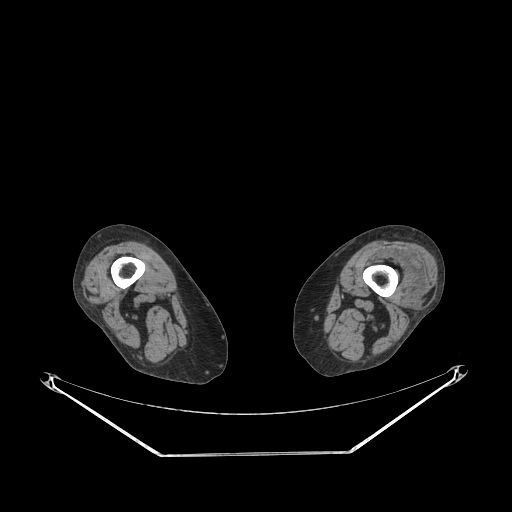
CT of an extremity soft-tissue mass (from a PET/CT study), one axial slice; slice 193 of 267 in the series (ordered by position); reconstruction kernel STANDARD; 140 kVp; soft-tissue window (W 400 / L 40 HU); 512 × 512 image matrix. Female patient. Case-level facts recorded for this patient, not image findings: histological type: undifferentiated – high grade; grade: high; site of the primary tumour: left thigh.
Structures marked on this image (expert contour drawn on MRI and transferred to this co-registered scan by the dataset authors):
- gross tumour volume including surrounding oedema: bounding box <377,253,426,296> (left, top, right, bottom; pixels)